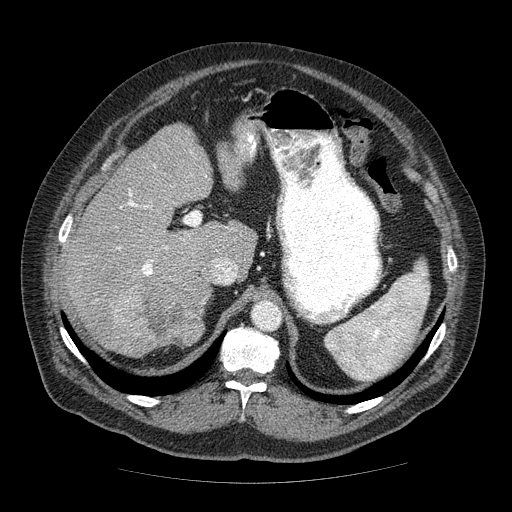
Contrast-enhanced abdominal CT (liver protocol), one axial slice; slice 40 of 85 in the series (ordered by position); 120 kVp; soft-tissue window (W 400 / L 40 HU); 2.5 mm slice thickness; 512 × 512 image matrix. From the clinical record (not read from this slice): diagnosis: hepatocellular carcinoma (patient treated with transarterial chemoembolisation; whether this scan precedes or follows treatment is not stated here); TNM stage (as recorded): Stage-IIIA; Child-Pugh class: A; tumour size: 7 cm.
Structures marked on this image (semi-automatic segmentation, software-assisted and operator-edited):
- liver parenchyma outside the tumour (the mass and vessels are separate outlines, so this box may not span the whole liver): bounding box [x1, y1, x2, y2] px = [64, 124, 256, 356]
- mass: [100, 273, 210, 358]
- liver vessels: [117, 164, 206, 276]